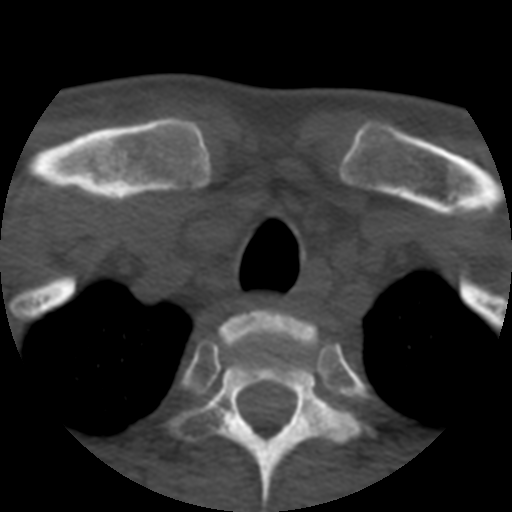
CT including the spine, one axial slice; position 435 of 508 along the scan axis; reconstruction kernel STANDARD; 120 kVp; bone window (W 1800 / L 400 HU); 1.25 mm slice thickness; 512 × 512 image matrix. Patient age 57 years. From the clinical record (not read from this slice): primary cancer: prostate.
Annotated regions visible in this slice (semi-automatic segmentation, software-assisted and operator-edited):
- T1 vertebra: box from (x=219, y=308) to (x=318, y=352) px
- T2 vertebra: (x=169, y=343)–(x=360, y=507)